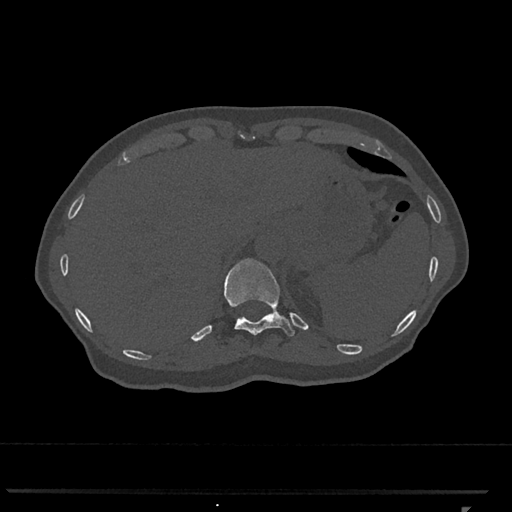
CT including the spine, one axial slice; position 516 of 793 along the scan axis; reconstruction kernel Br40s/3; 120 kVp; bone window (W 1800 / L 400 HU); 512 × 512 image matrix. Female patient, age 62 years. Case-level facts recorded for this patient, not image findings: primary cancer: renal.
Annotated regions visible in this slice (semi-automatically segmented with operator editing):
- T11 vertebra: bounding box <224,258,295,336> (left, top, right, bottom; pixels)